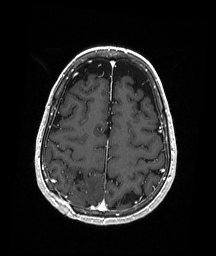
Brain MRI from a brain-tumour surgery series, one axial slice. T1-weighted post-contrast. 1 mm slice thickness. 216 × 256 image matrix, field of view 211 × 250 mm. Case-level facts recorded for this patient, not image findings: histopathology: Astrocytoma; WHO grade: 3; IDH mutation: yes; tumour location: Right Parietal.
Structures marked on this image (outlined manually by an expert reader):
- previous resection cavity: bounding box (x1, y1, x2, y2) in pixels: (73, 171, 84, 191)